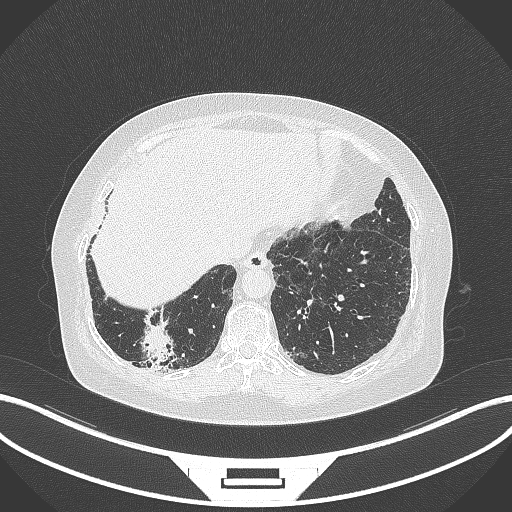
Chest CT, one axial slice; slice 30 of 296 in the series (ordered by position); lung window (W 1500 / L -600 HU); 1 mm slice thickness; 512 × 512 image matrix, field of view 400 × 400 mm. Female patient, age 65 years. Case-level facts recorded for this patient, not image findings: clinical TNM (as recorded): T2b N1 M0.
Structures marked on this image (bounding box drawn by a radiologist):
- lung tumour (recorded histology: adenocarcinoma): box from (x=139, y=317) to (x=179, y=365) px